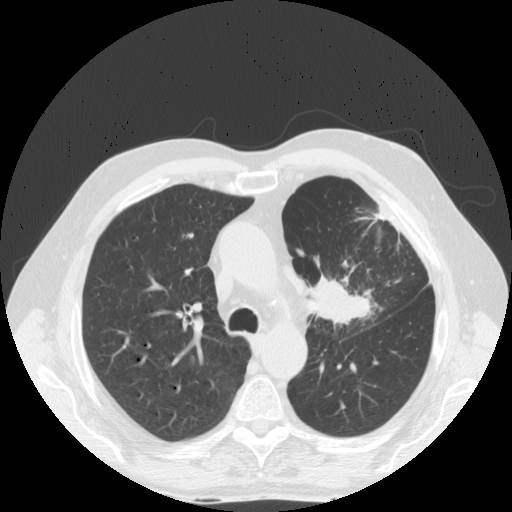
Chest CT (low-dose screening protocol), one axial image; first (baseline) screen; lung window (W 1500 / L -600 HU); 2.5 mm slice thickness; slice 52 of 171 in the series; 512 × 512 image matrix. Male, age 70 years at enrolment. Former smoker at enrolment.
Expert reader's lesion annotation, box from (x=294, y=255) to (x=390, y=344) px. Reader record for this screening exam (exam-level; its link to the box is not recorded): non-calcified nodule or mass ≥4 mm, left upper lobe, 46 × 31 mm, spiculated (stellate) margins, soft tissue attenuation. Official screen result: positive, change unspecified: nodule(s) >= 4 mm or enlarging nodule(s), mass(es), or other non-specific abnormalities suspicious for lung cancer. Participant outcome: lung cancer diagnosed 78 days after this screen — squamous cell carcinoma, NOS, left upper lobe, poorly differentiated (G3), stage IIIB (AJCC 6th edition), 46 mm at pathology.